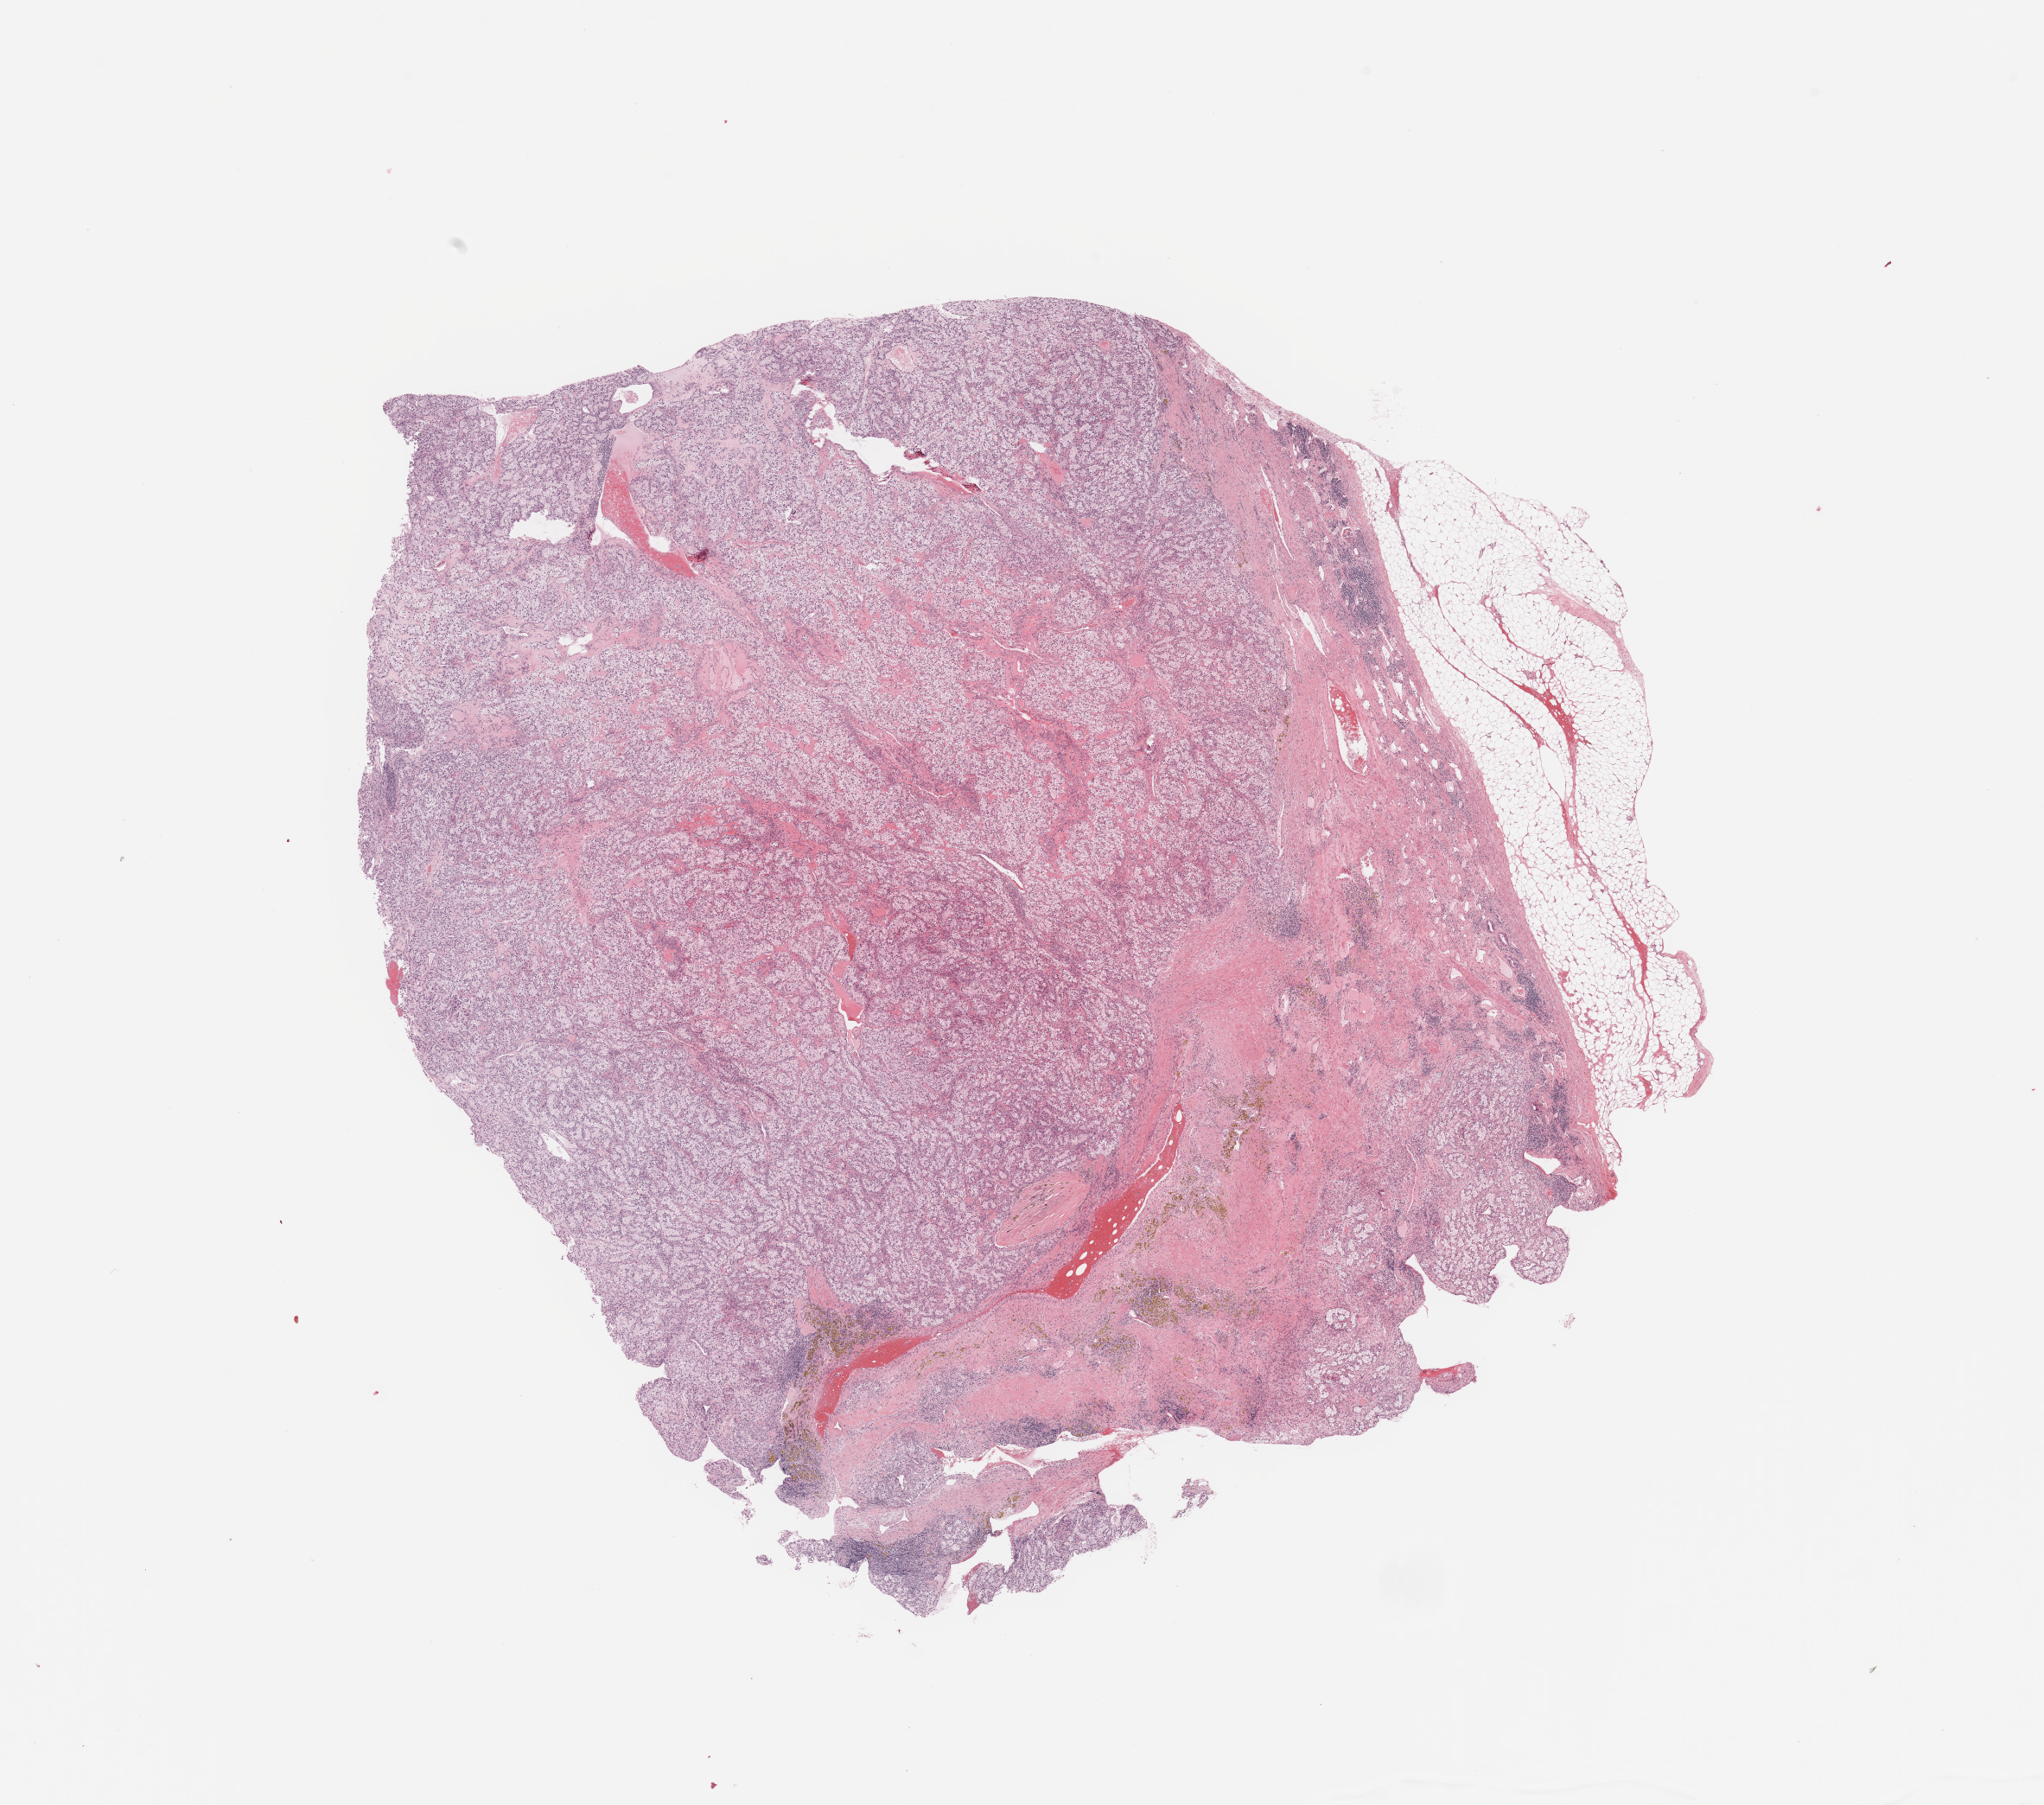
Digitized H&E-stained tissue section (whole slide) — whole scanned area (about 18.7 x 16.5 mm) shown as a low-resolution overview. Tumour tissue sample, sampled site: kidney. Patient: male, age 67 years. Histologic grade: G3 (poorly differentiated). Slide review estimates, as recorded: tumour nuclei 80%, necrosis 5%.
Diagnosis: Renal cell carcinoma, NOS. AJCC pathologic stage: IV.